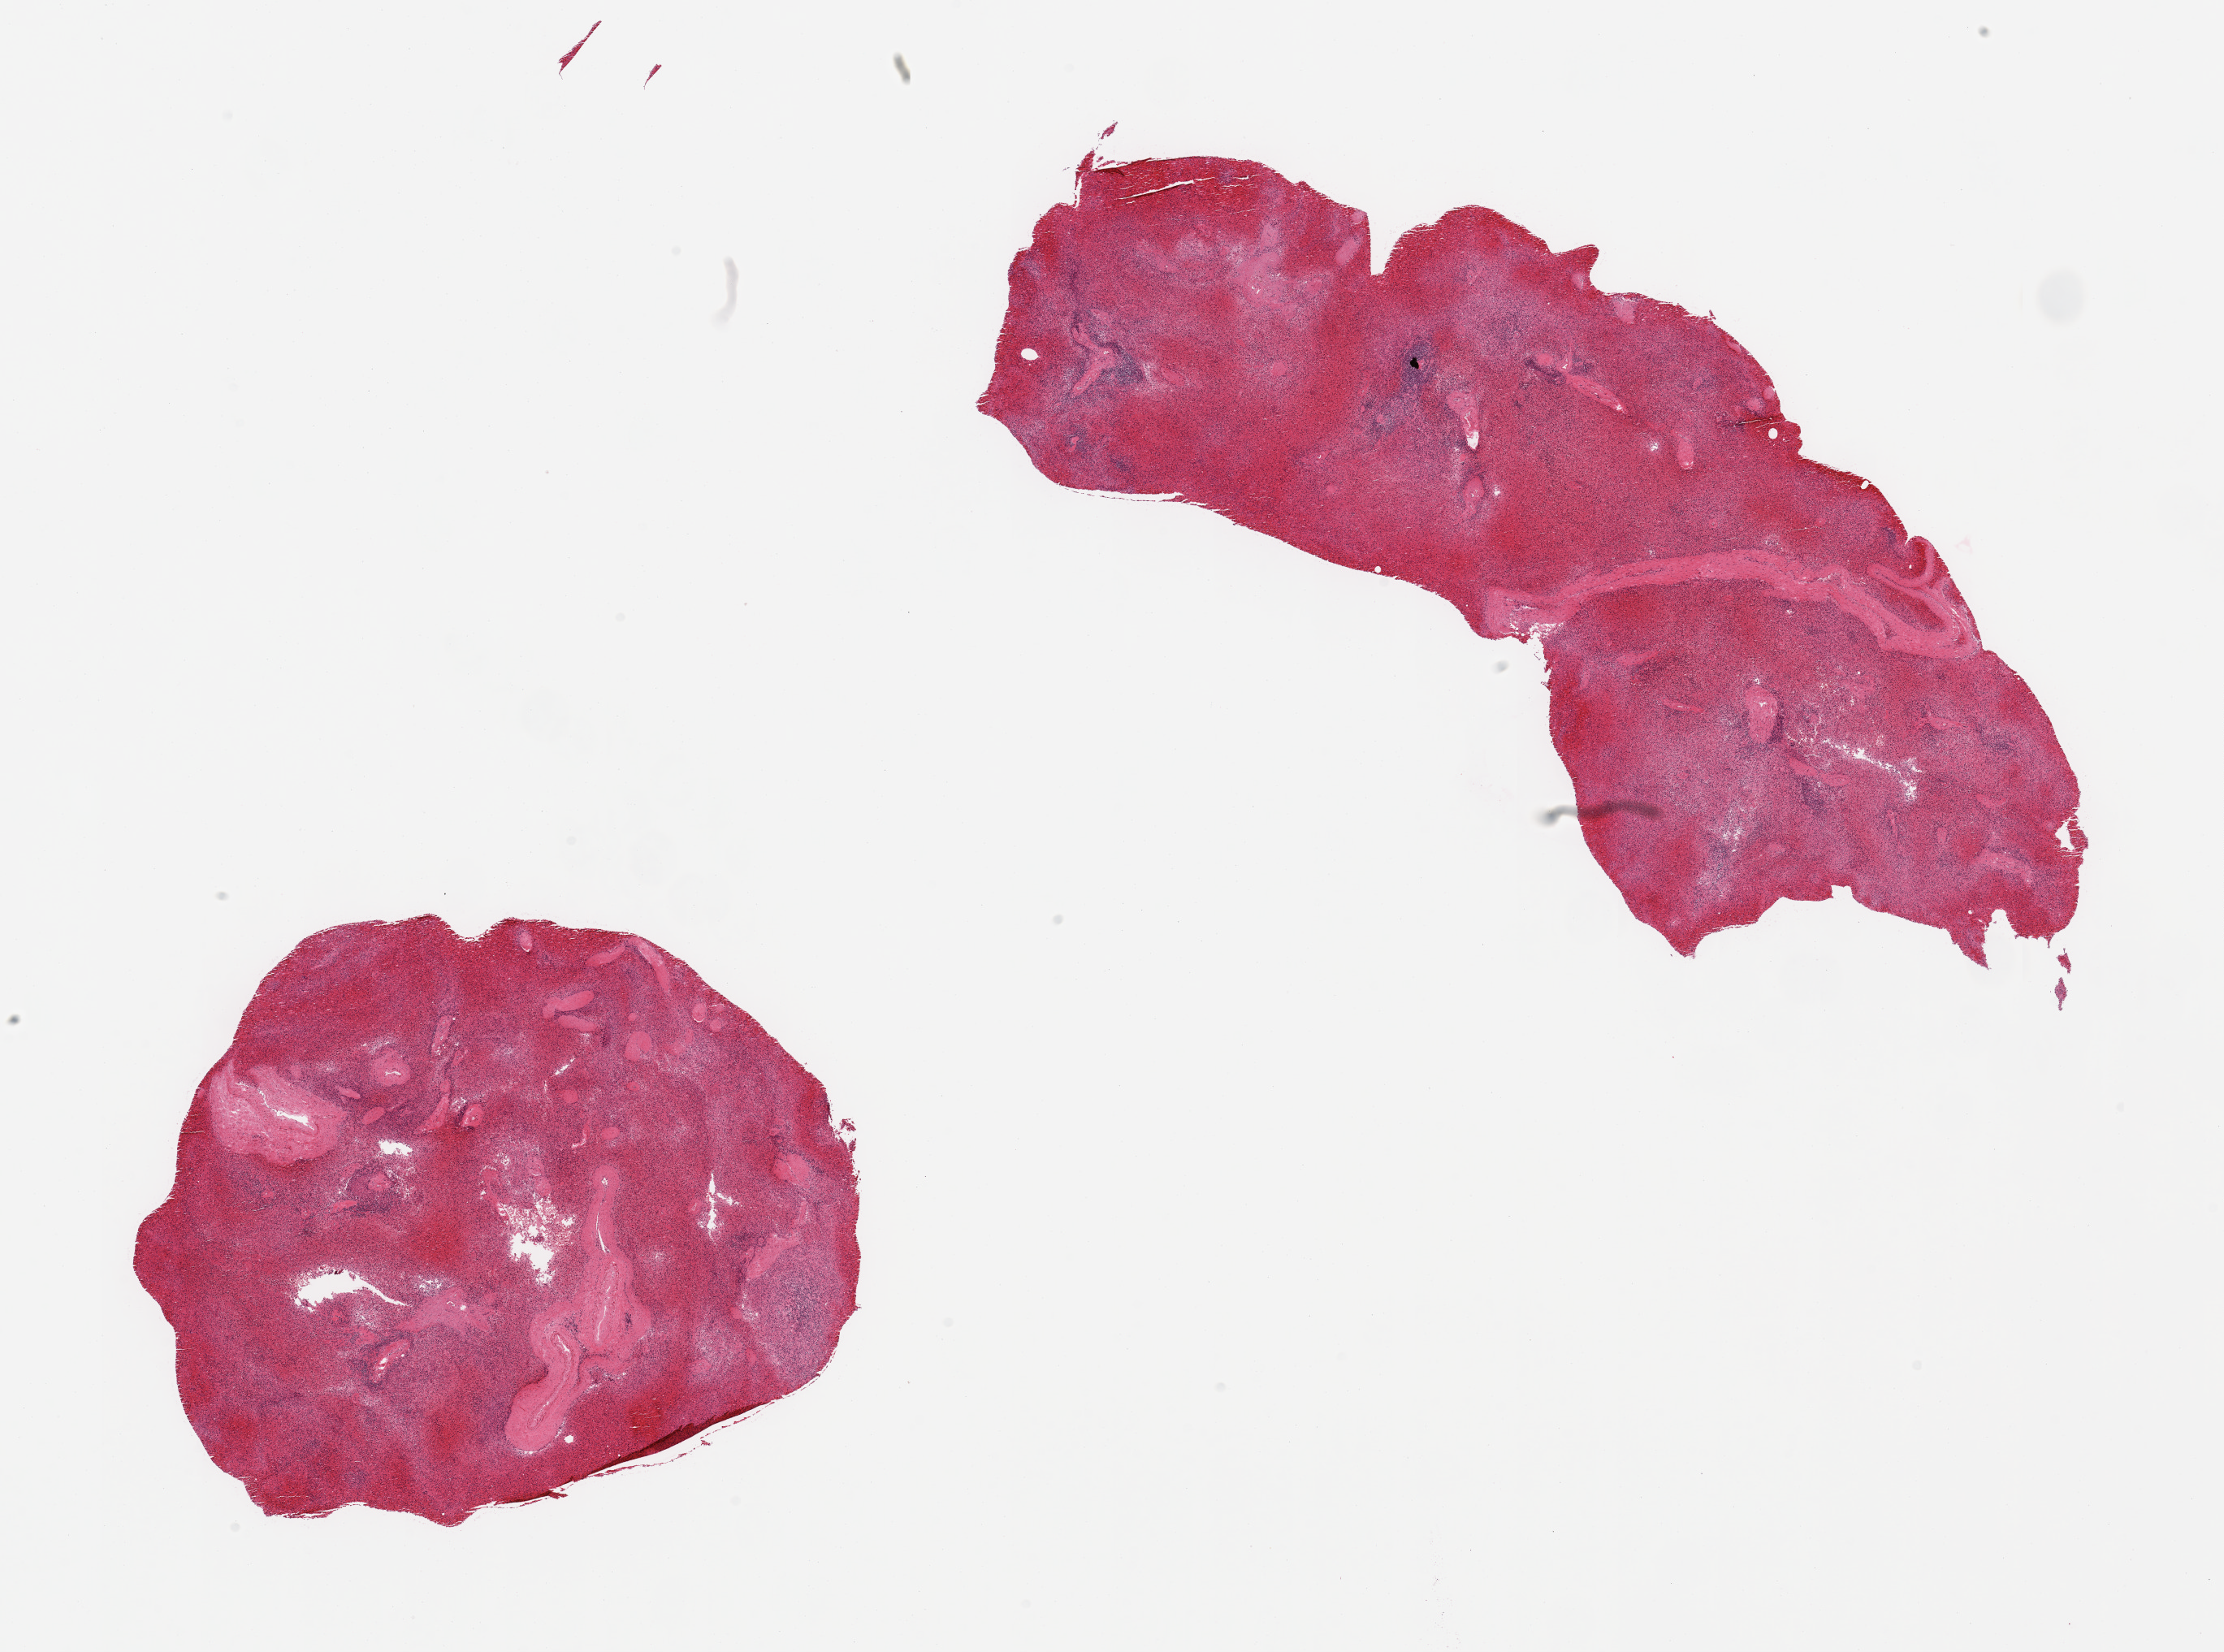
H&E whole-slide image, brightfield, low-resolution overview of the scanned area, about 21.7 x 16.1 mm (acquisition: 20x scan). PAXgene-fixed paraffin-embedded (PFPE) section. Section of spleen (target tissue). Donor tissue sample. Male donor.
Pathologist's review note for this sample: 2 pieces; heavily congested.